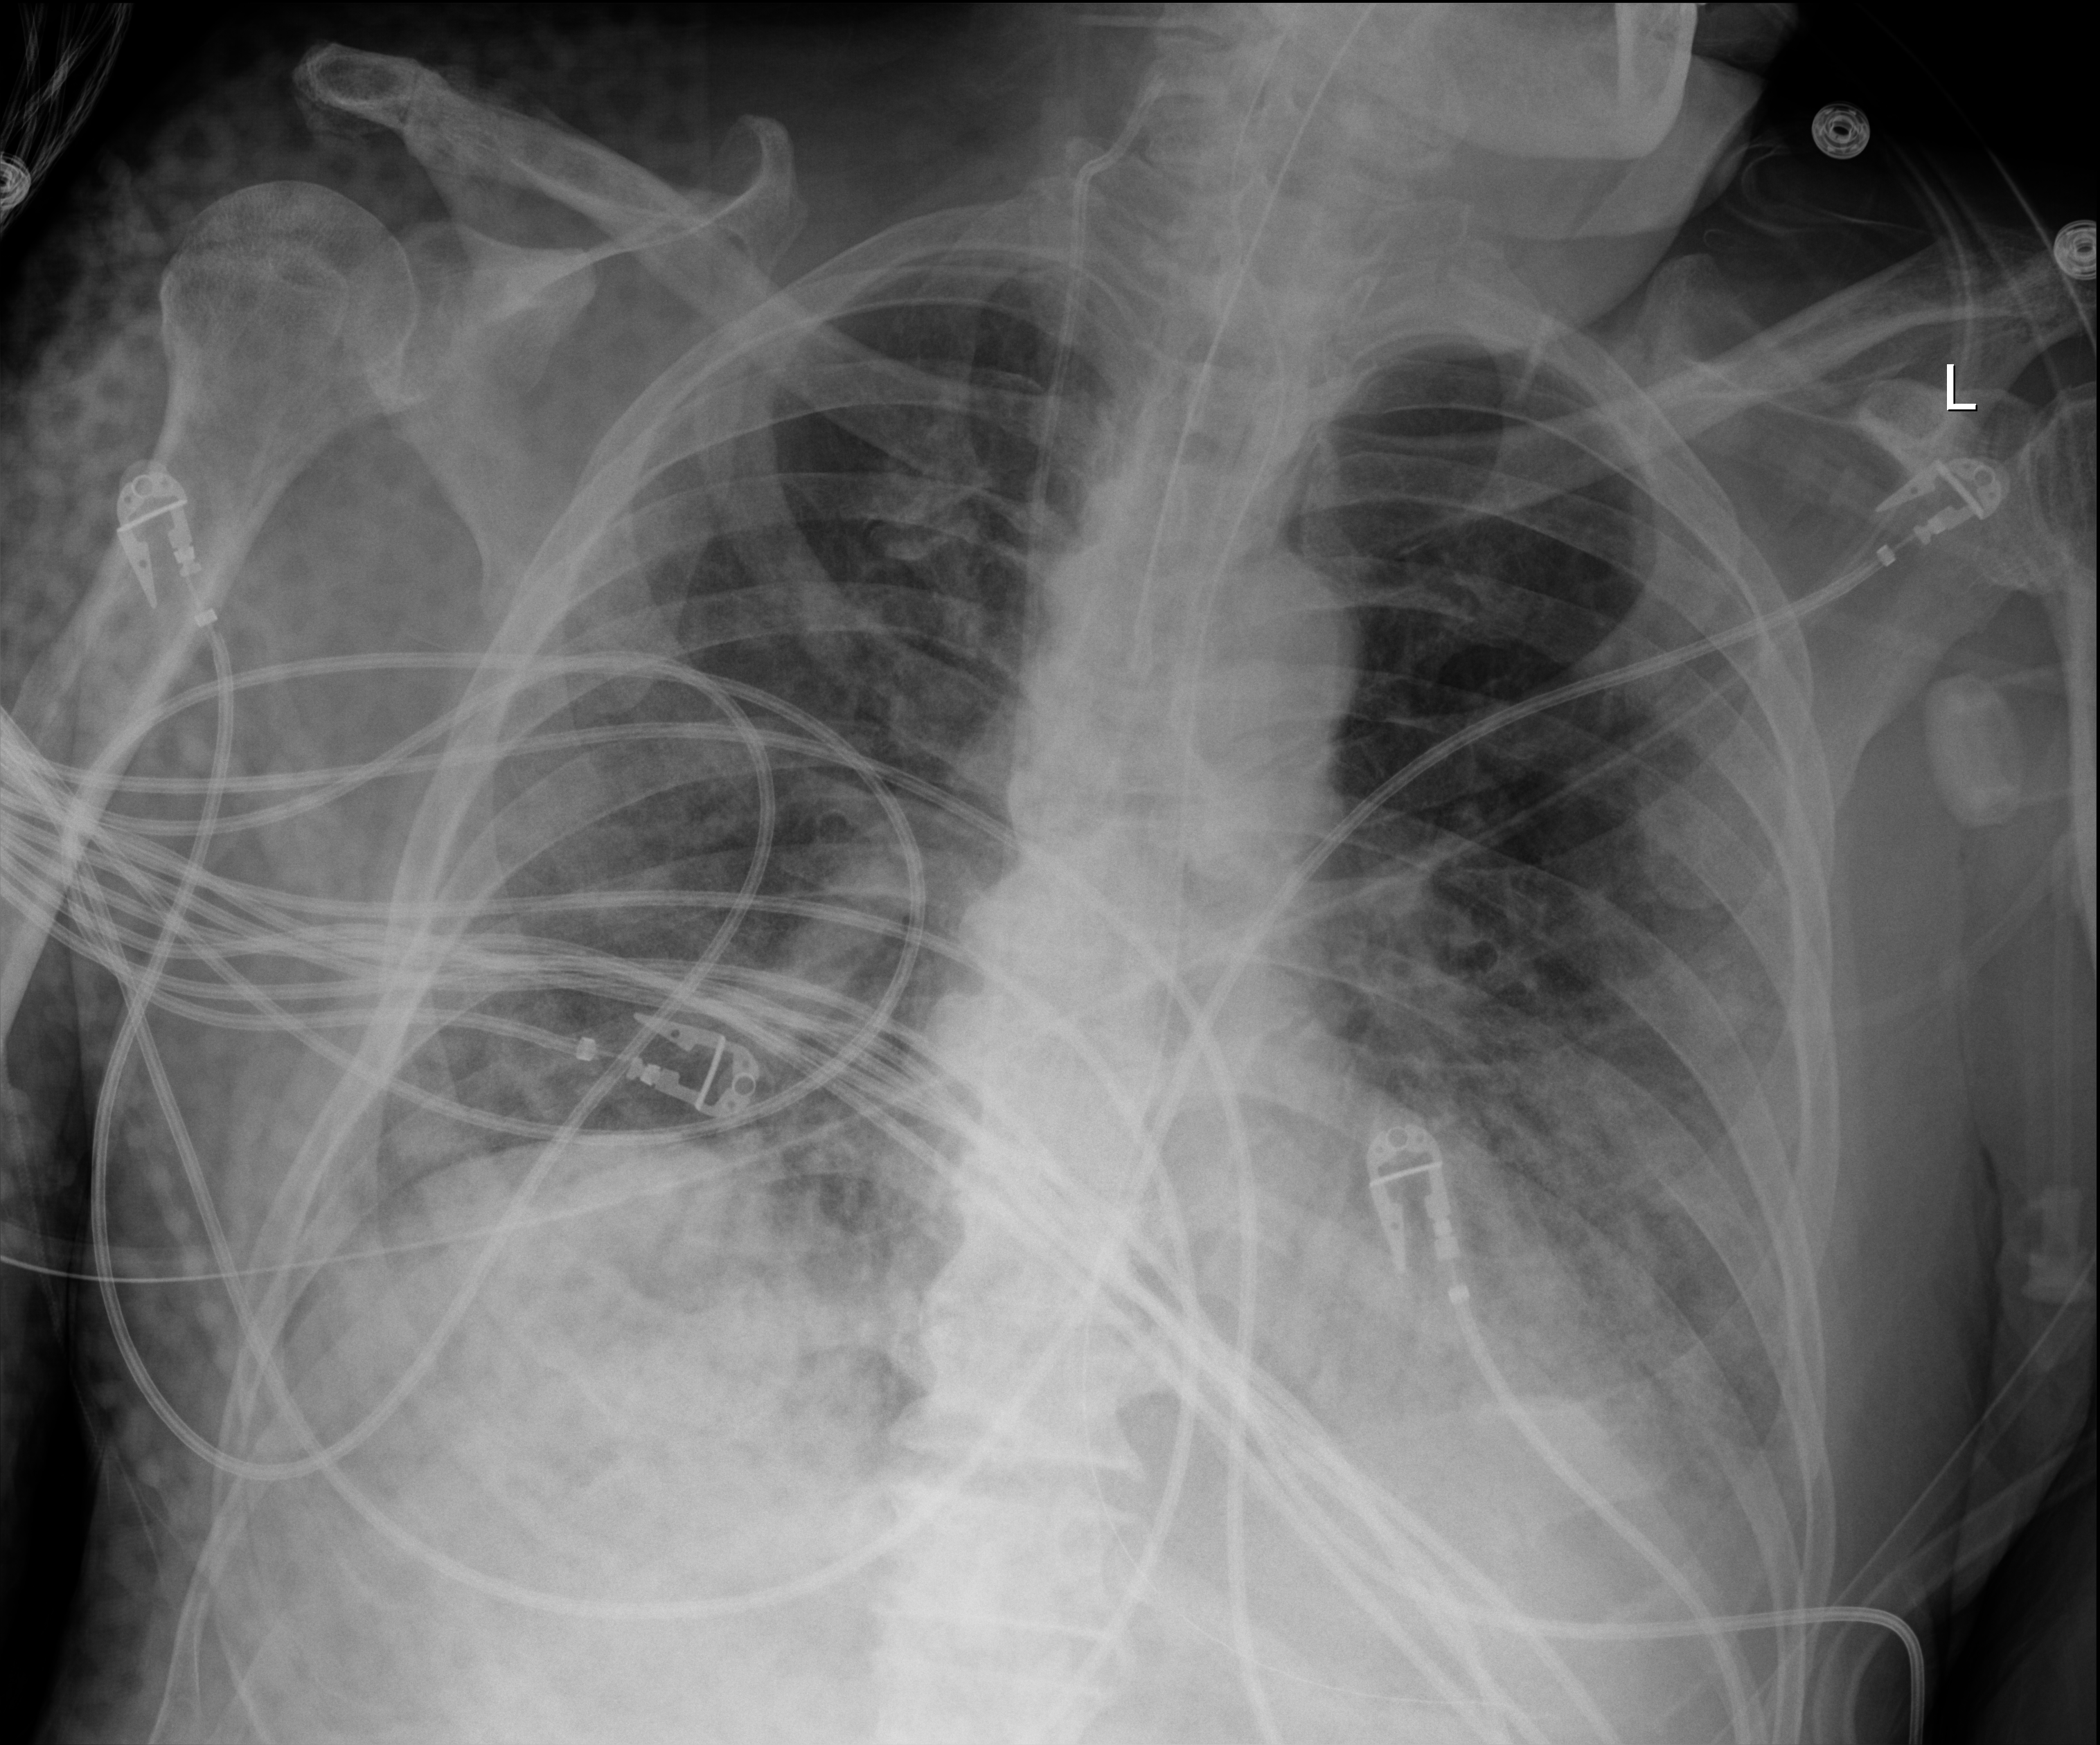
Bedside chest radiograph (digital radiography); anteroposterior (AP) projection. Male patient hospitalised with COVID-19, age 75–90 years.
From the hospital-stay record, not from the radiograph (when in the stay this image was taken is not recorded): length of hospital stay: 33 days; mechanically ventilated during this hospital stay: yes; other chronic lung disease (admission record): no.